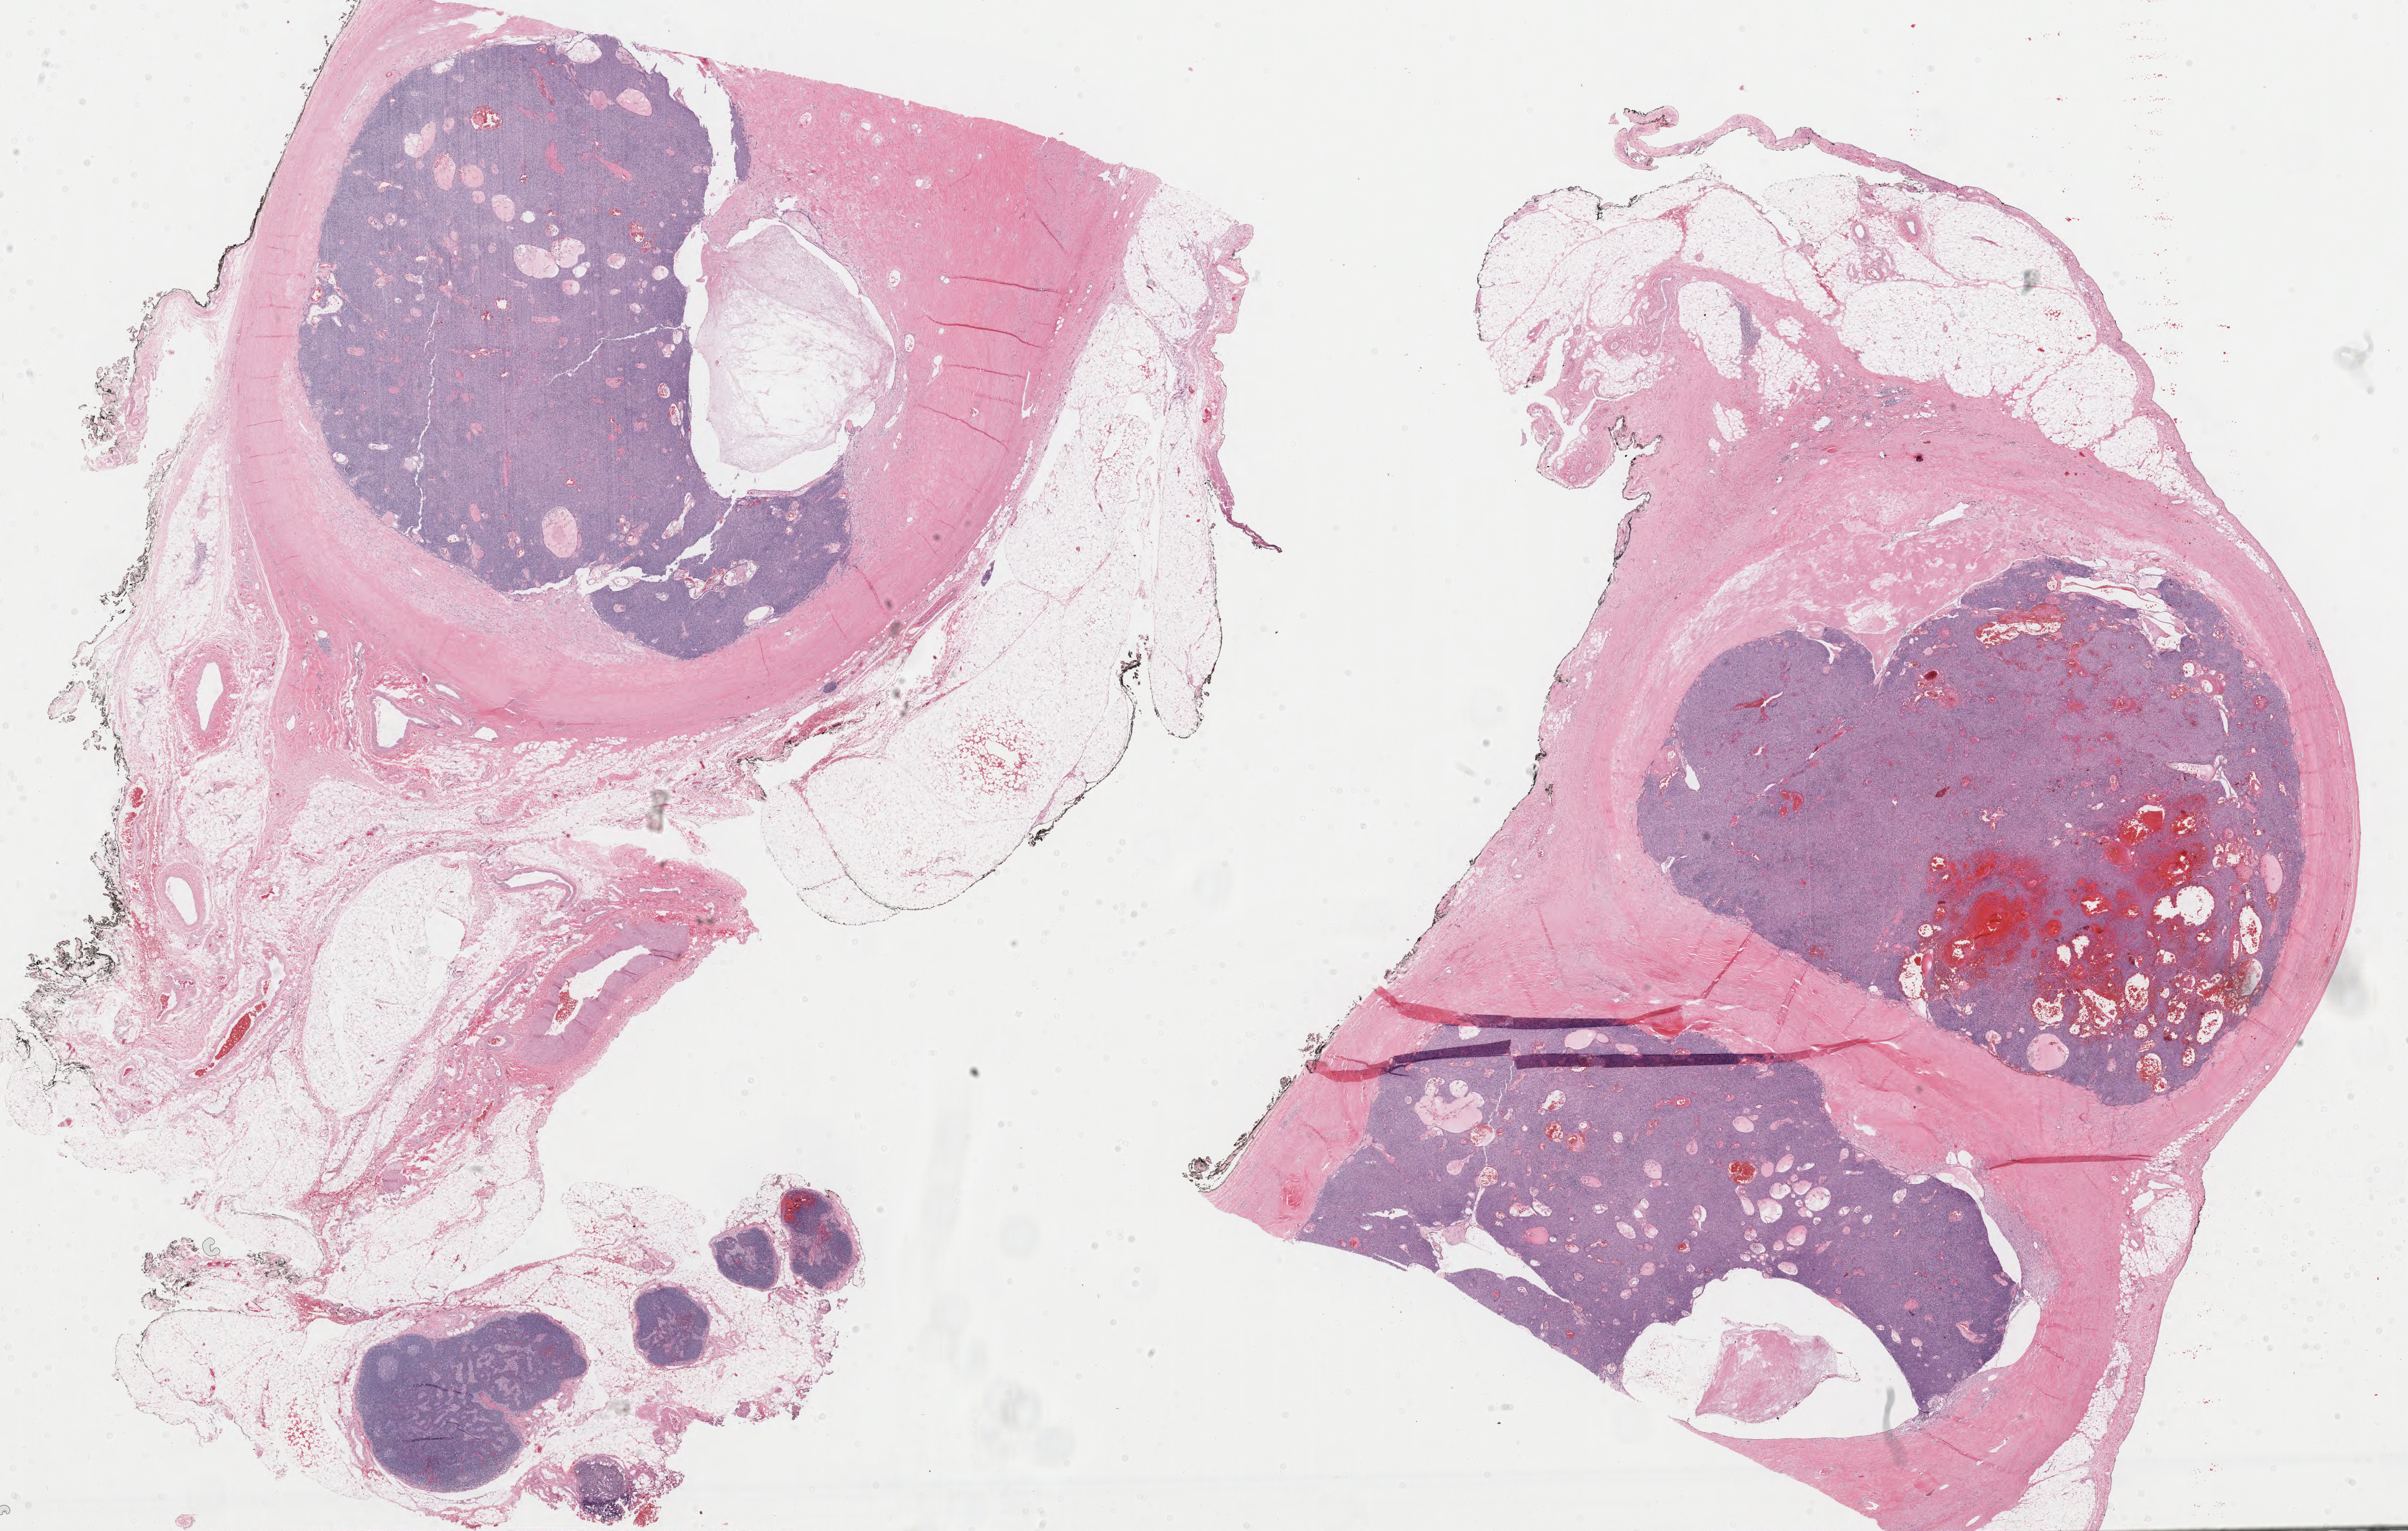
Digitized Hematoxylin and eosin (H&E) stained tissue section (whole slide), a low-resolution overview of the entire scanned area, about 30.8 x 19.6 mm; formalin-fixed paraffin-embedded (FFPE) diagnostic section; primary tumour sample from the thymus. Female, age 43 years at initial diagnosis.
- diagnosis: Thymoma, type B2, malignant